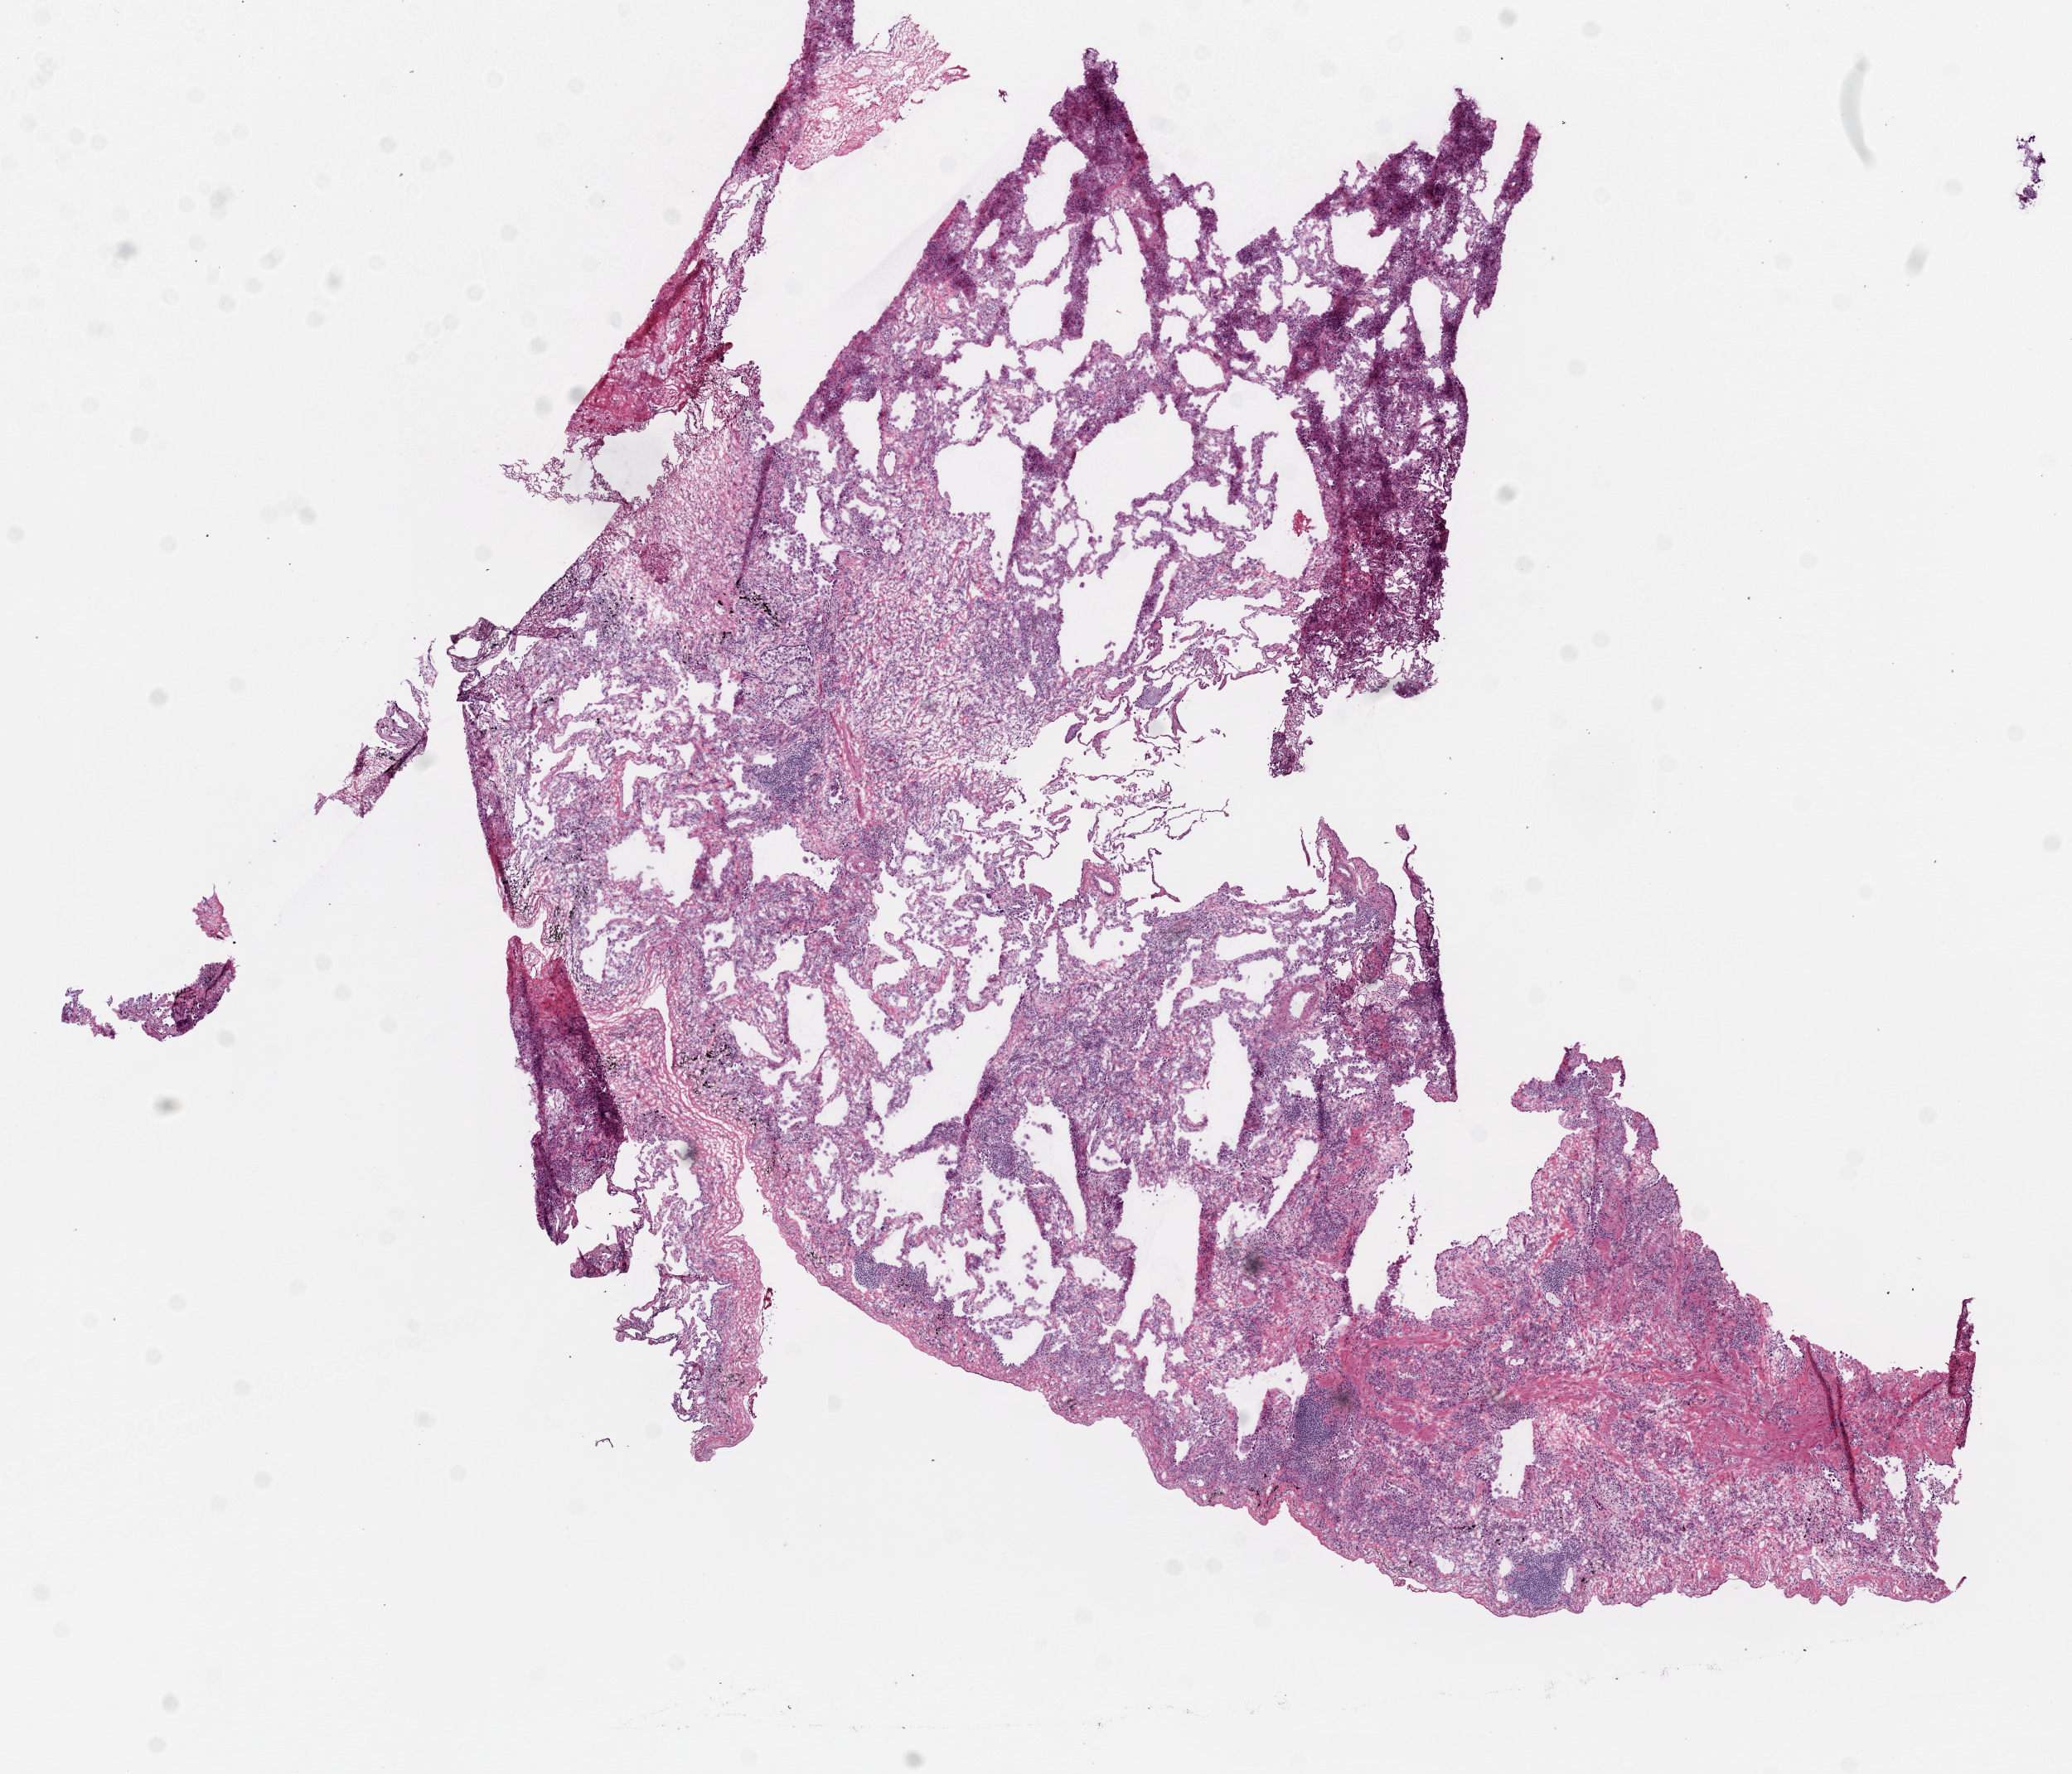
Digitized H&E tissue section (whole slide), whole scanned area (about 10.0 x 8.6 mm) shown as a low-resolution overview. Frozen section from the bottom of the tissue portion. Sample: solid tissue normal (non-tumour tissue), lung. Patient: male, age at initial diagnosis 80 years.
This section: solid tissue normal sample (biorepository sample class). Patient diagnosis: Squamous cell carcinoma, NOS (lower lobe, lung).